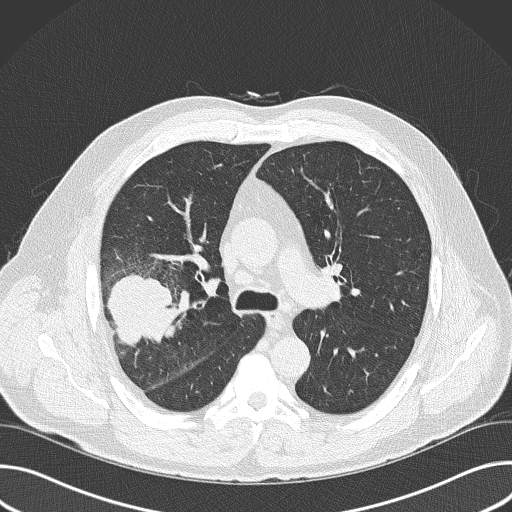
Low-dose screening chest CT, axial slice, baseline screening round, lung window (W 1500 / L -600 HU), 2 mm slice thickness, lung (sharp) reconstruction kernel (B50f), slice 105 of 157 in the series. Male participant, aged 56 years at enrolment.
• Lesion marked by an expert reader, bounding box <82,263,187,371> (left, top, right, bottom; pixels).
• Screening reader's record for this exam (one nodule recorded; not confirmed to be the boxed lesion): non-calcified nodule or mass ≥4 mm, right upper lobe, 6 × 5 mm, spiculated (stellate) margins, soft tissue attenuation.
• Participant outcome: lung cancer diagnosed 16 days after this screen — adenocarcinoma, NOS, right upper lobe, poorly differentiated (G3), stage IIB (AJCC 6th edition), 60 mm at pathology.